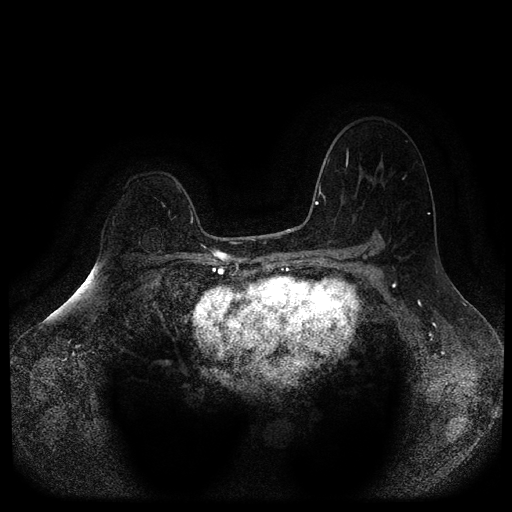
Breast MRI (dynamic contrast-enhanced, multi-phase), one axial slice; position 72 of 116 along the scan axis; dynamic contrast-enhanced series, time point 2 of 5 at this slice position (early post-contrast); 1.5 T; TE 2.6 ms, TR 5.4 ms; 2 mm slice thickness; 512 × 512 image matrix, field of view 340 × 340 mm. Female patient, age 64 years.
Structures marked on this image (semi-automatically segmented with operator editing):
- breast lesion (labelled benign in the annotation): bounding box (x1, y1, x2, y2) in pixels: (139, 227, 164, 255)